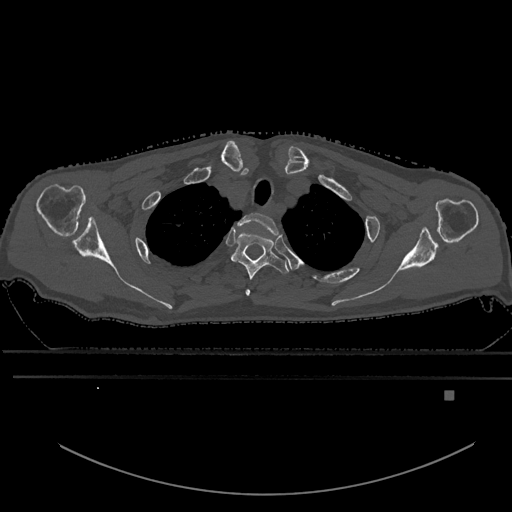
CT including the spine, one axial slice. Position 500 of 969 along the scan axis. Bone window (W 1800 / L 400 HU). 512 × 512 image matrix. Patient: male, 82 years. From the clinical record (not read from this slice): primary cancer: prostate; vertebrae with lytic lesions (as recorded): T11, T9, T8, T2.
Outlined on this slice (semi-automatically segmented with operator editing):
- T1 vertebra: box from (x=237, y=212) to (x=279, y=234) px
- T2 vertebra: (x=231, y=232)–(x=289, y=295)